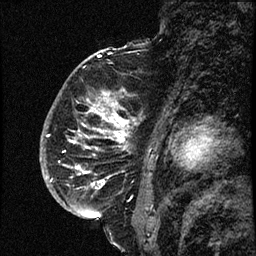
Breast MRI (dynamic contrast-enhanced), one sagittal slice; position 47 of 66 along the scan axis; dynamic contrast-enhanced study with each time point stored as its own series, time point 2 of 3 at this slice position (early post-contrast, ordered by acquisition time); 1.5 T; TE 4.2 ms, TR 17.6 ms; 256 × 256 image matrix, field of view 200 × 200 mm. Female patient. From the clinical record (not read from this slice): setting: breast cancer imaged before/during neoadjuvant chemotherapy; receptor status: HER2-positive.
Outlined on this slice (semi-automatically segmented with operator editing):
- analysis volume of interest (the breast-tissue region the enhancement analysis was run in; not a lesion): bounding box <52,69,140,209> (left, top, right, bottom; pixels)
- tumour enhancement mask (voxels above the 100 % enhancement threshold inside the analysis volume of interest): <73,91,138,207>